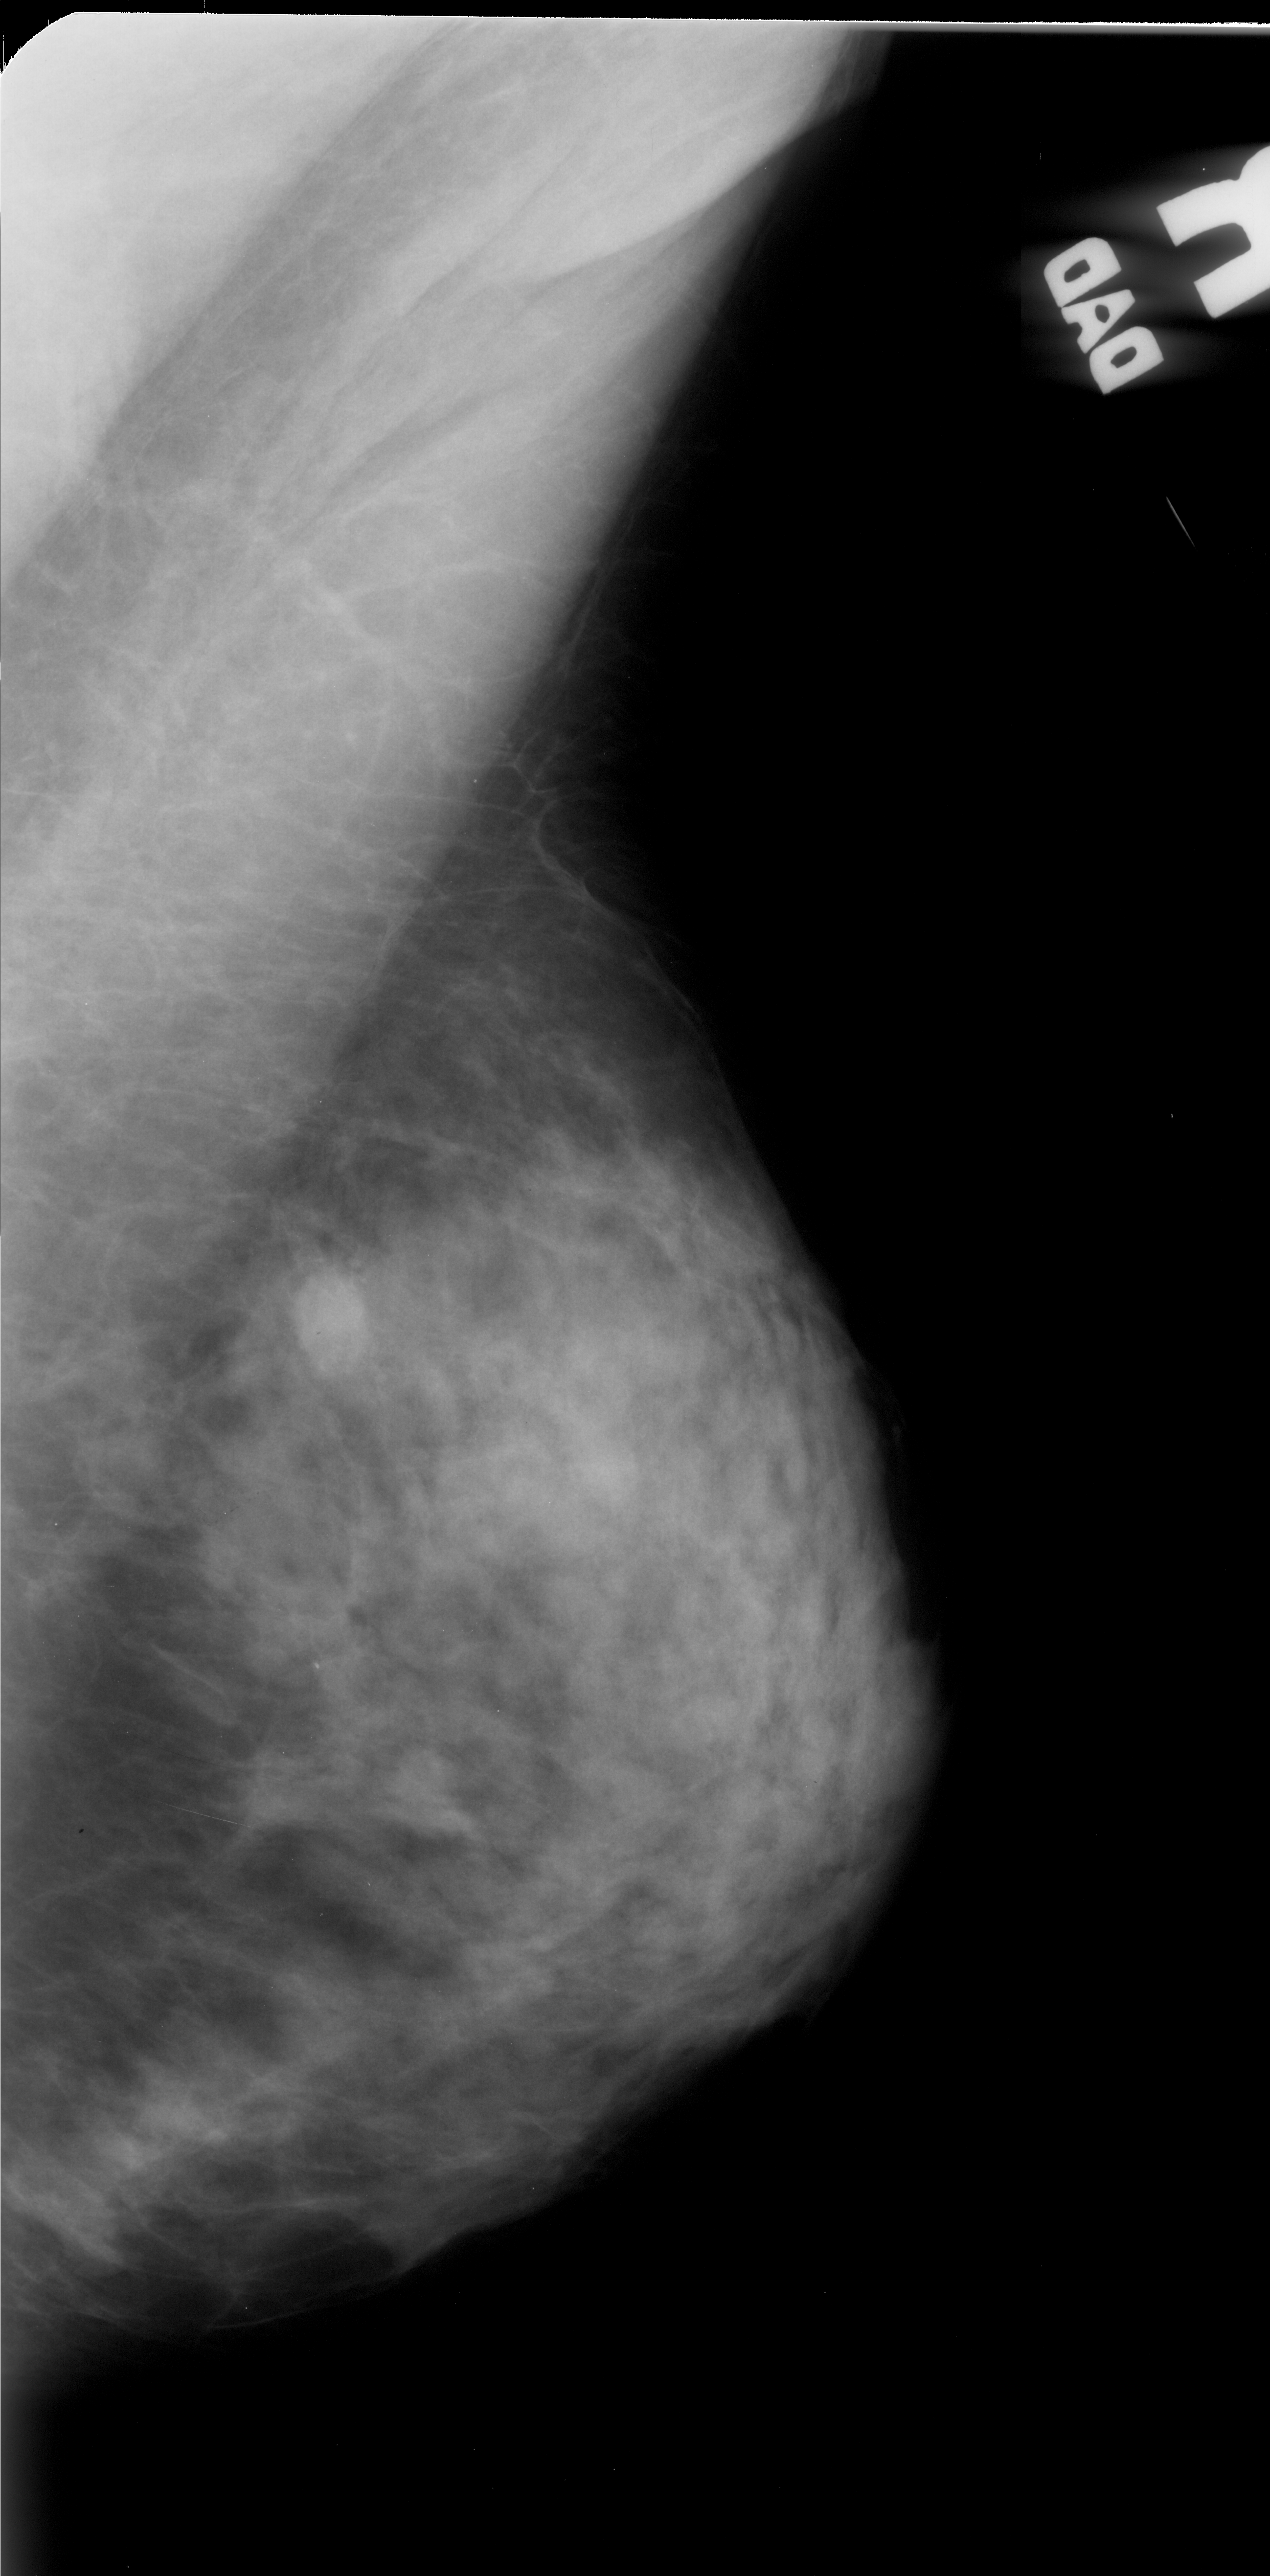
Mammogram (digitized film); right breast; MLO view; breast composition: heterogeneously dense (BI-RADS density category 3 of 4).
Finding: mass, shape oval, margins ill defined; BI-RADS assessment category 4; subtlety rating 4 on a 1 (subtle) to 5 (obvious) scale; pathology result (as recorded, not read from the image): malignant.